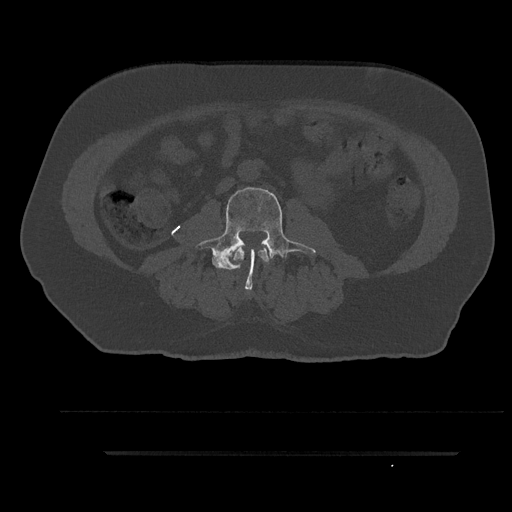
CT including the spine, one axial slice. Slice 50 of 797 in the series (ordered by position). Reconstruction kernel Br40s/3. 120 kVp. Bone window (W 1800 / L 400 HU). 0.5 mm slice thickness. 512 × 512 image matrix, field of view 432 × 432 mm. Patient: male, 63 years. Case-level facts recorded for this patient, not image findings: primary cancer: renal.
Structures marked on this image (semi-automatic segmentation, software-assisted and operator-edited):
- L2 vertebra: bounding box (x1, y1, x2, y2) in pixels: (233, 247, 269, 269)
- L3 vertebra: (195, 185, 316, 290)